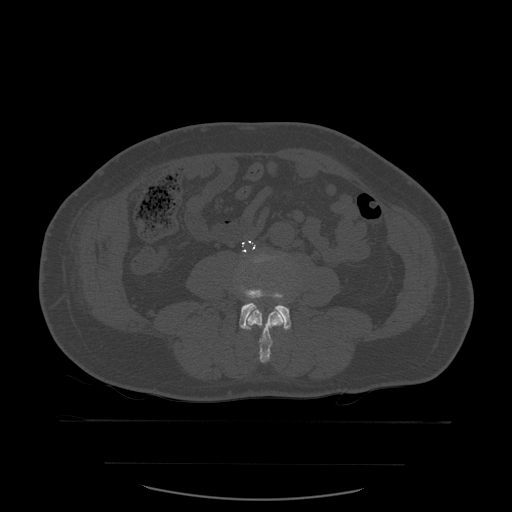
CT including the spine, one axial slice. Bone window (W 1800 / L 400 HU). 512 × 512 image matrix, field of view 479 × 479 mm. Patient age 71 years. From the clinical record (not read from this slice): primary cancer: lung; vertebrae with lytic lesions (as recorded): T1, T2, L5, S1.
Outlined on this slice (semi-automatic segmentation, software-assisted and operator-edited):
- L3 vertebra: bounding box <248,310,285,363> (left, top, right, bottom; pixels)
- L4 vertebra: <240,290,292,330>